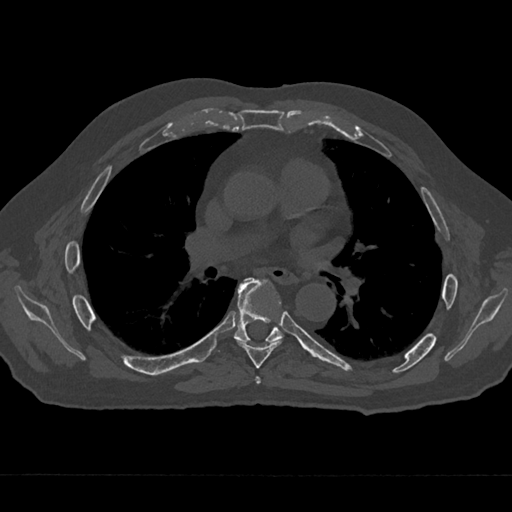
CT including the spine, one axial slice; position 399 of 797 along the scan axis; reconstruction kernel Br40s/3; bone window (W 1800 / L 400 HU); 0.5 mm slice thickness; 512 × 512 image matrix. Male patient, age 75 years. From the clinical record (not read from this slice): primary cancer: renal; vertebrae with lytic lesions (as recorded): T4.
Structures marked on this image (semi-automatic segmentation, software-assisted and operator-edited):
- T5 vertebra: bounding box [x1, y1, x2, y2] px = [255, 376, 261, 385]
- T6 vertebra: [237, 305, 282, 368]
- T7 vertebra: [234, 278, 283, 343]